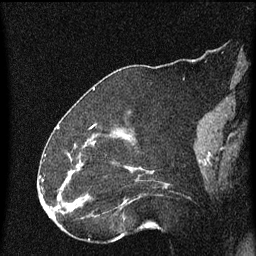
Breast MRI (dynamic contrast-enhanced), one sagittal slice; slice 25 of 60 in the series (ordered by position); dynamic contrast-enhanced series, image 2 of 4 at this slice position (ordered by acquisition); 1.5 T; TE 4.2 ms, TR 8 ms; 2 mm slice thickness; 256 × 256 image matrix, field of view 180 × 180 mm. Patient: female, 52 years.
Annotated regions visible in this slice (semi-automatically segmented with operator editing):
- analysis volume of interest (the breast-tissue region the enhancement analysis was run in; not a lesion): bounding box <73,148,170,219> (left, top, right, bottom; pixels)
- tumour enhancement mask (voxels above the 70 % enhancement threshold inside the analysis volume of interest): <73,170,125,207>